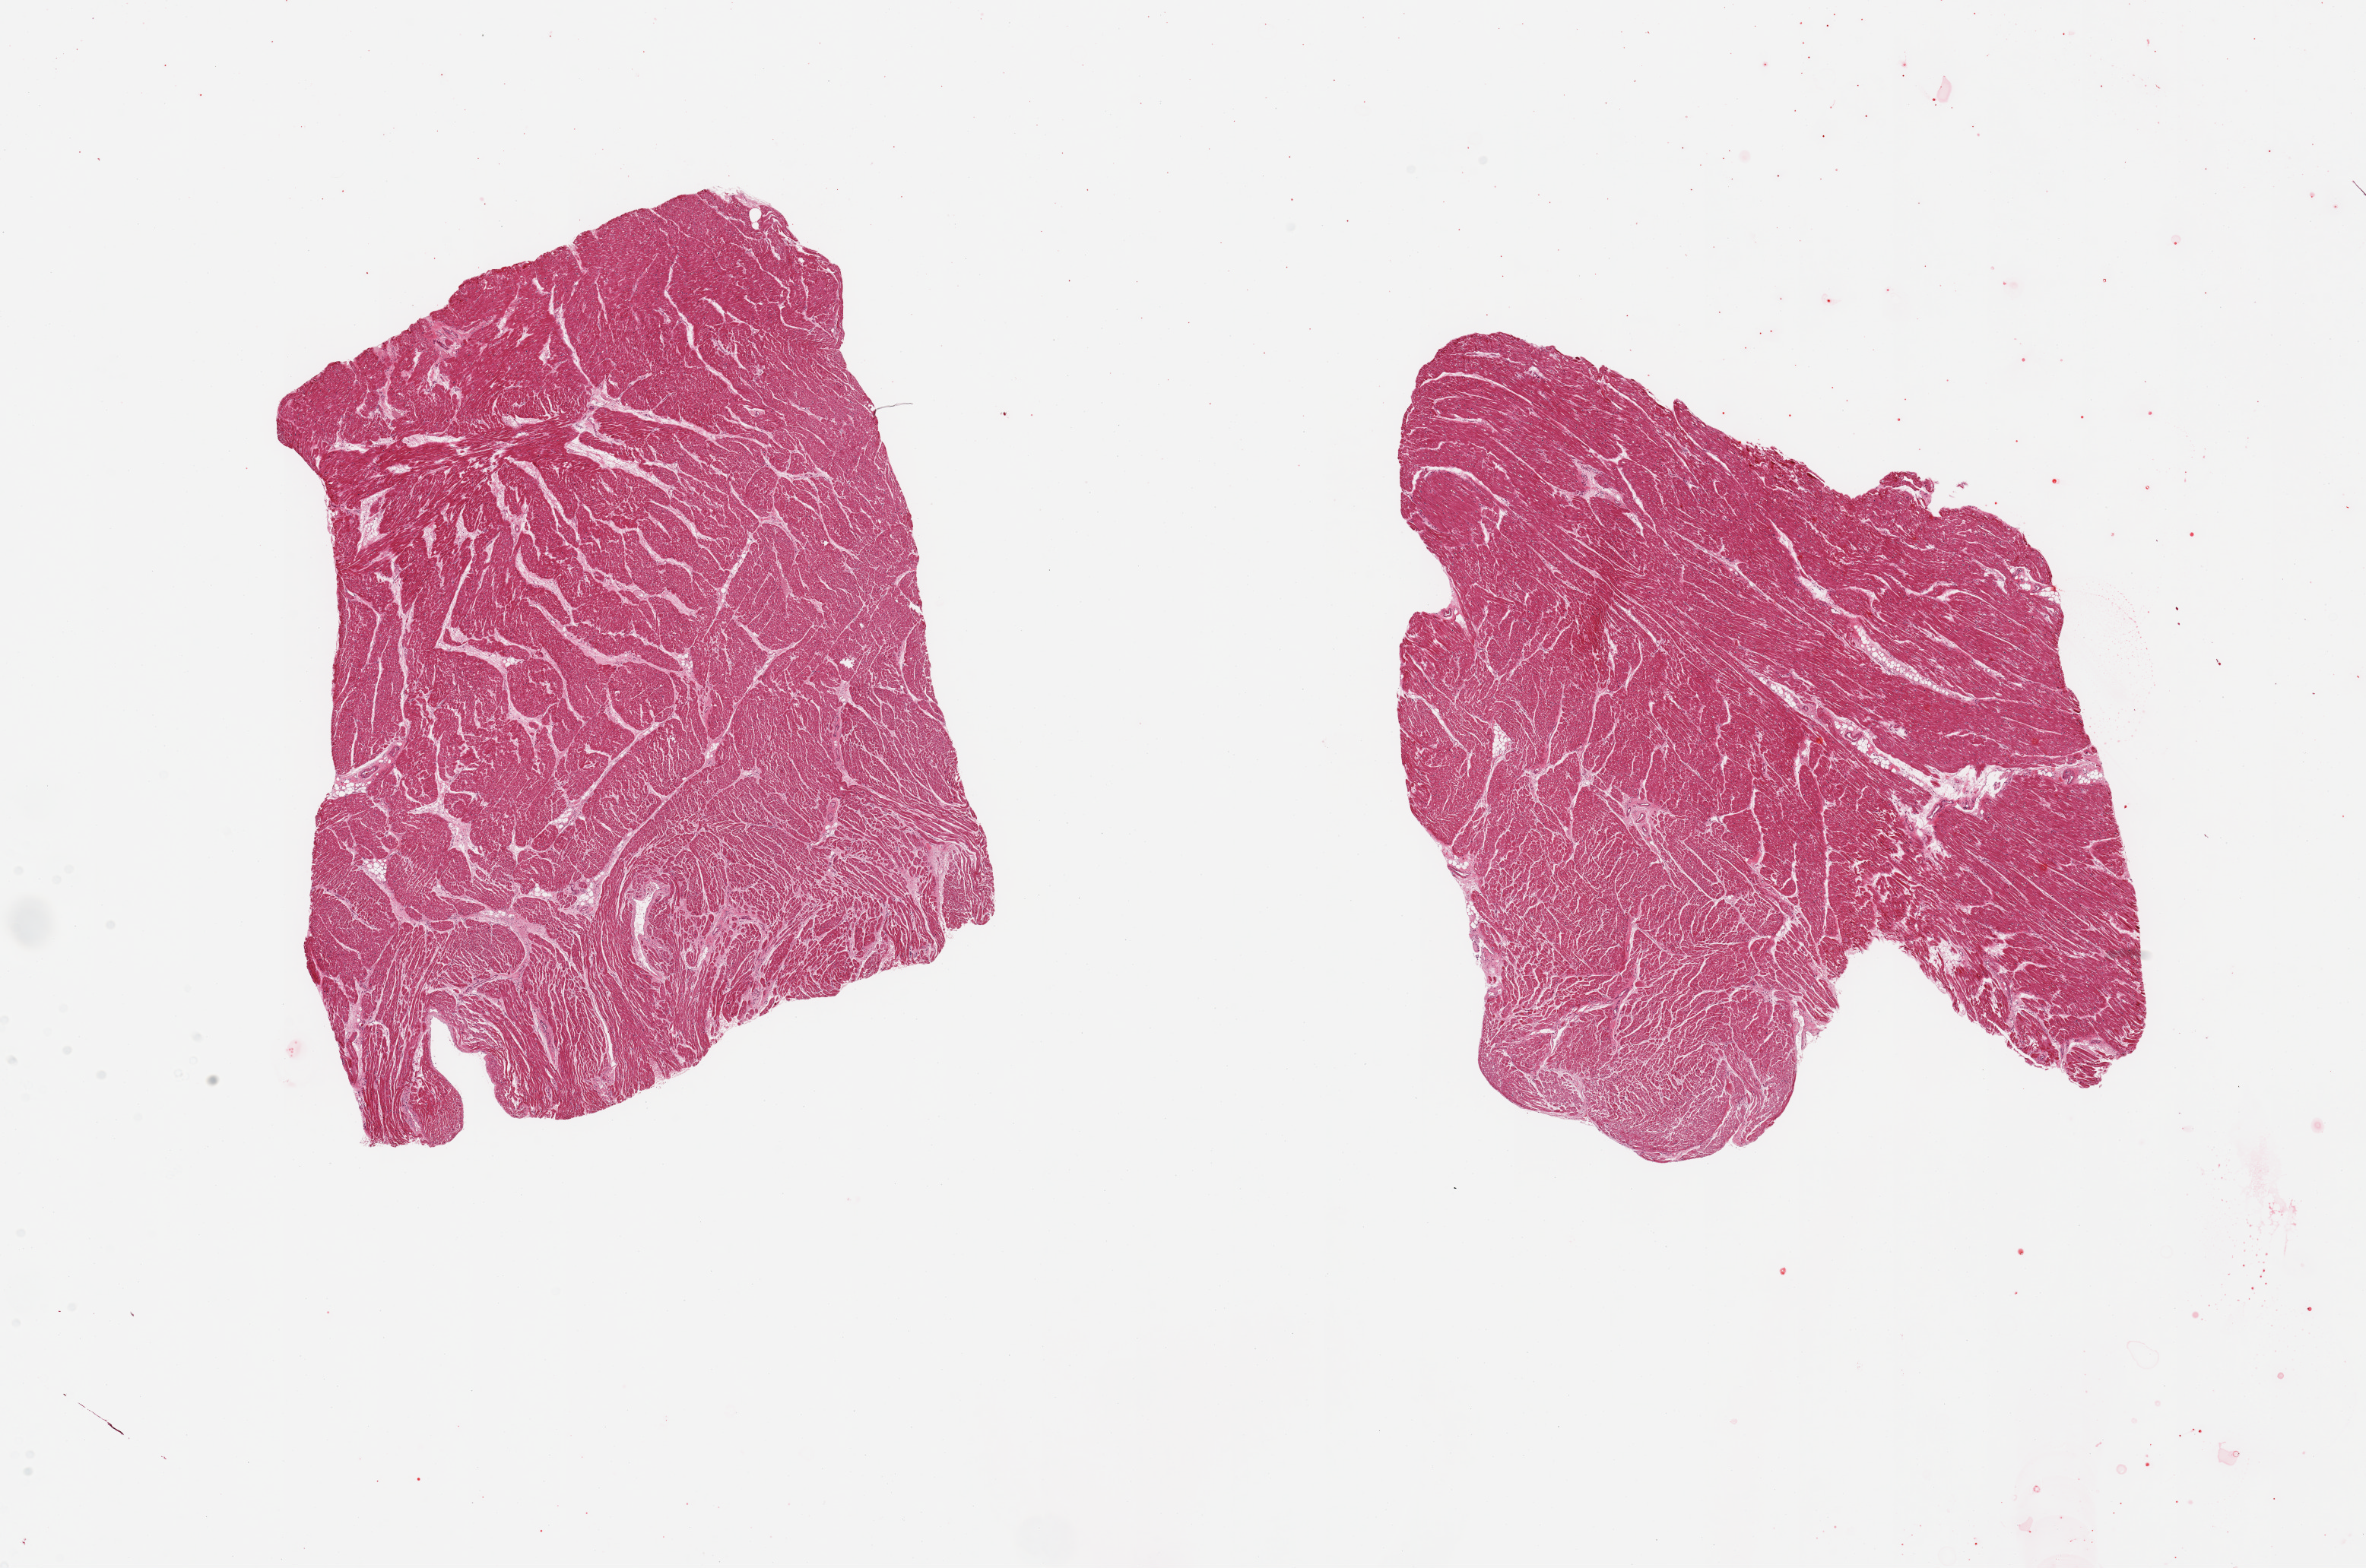
Whole-slide image, hematoxylin and eosin (H&E) stain, brightfield — low-resolution overview of the scanned area, about 24.6 x 16.3 mm (slide scanned at 20x). PAXgene-fixed paraffin-embedded (PFPE) section. Sampled site (target tissue): heart. Donor tissue sample. Donor sex: male.
- review note (as recorded): 2 pieces